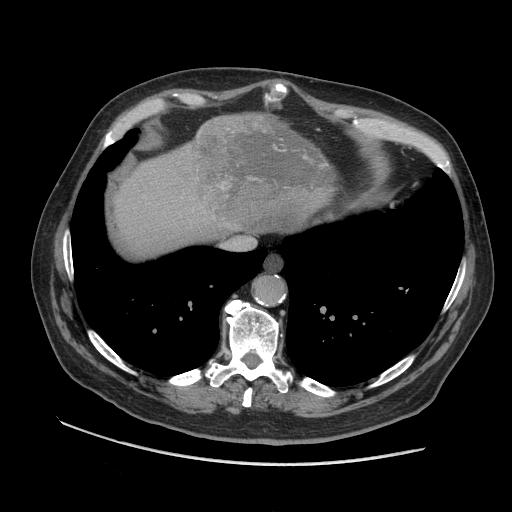
Contrast-enhanced abdominal CT (liver protocol), one axial slice; position 89 of 109 along the scan axis; 140 kVp; soft-tissue window (W 400 / L 40 HU); 2.5 mm slice thickness; 512 × 512 image matrix, field of view 420 × 420 mm. Case-level facts recorded for this patient, not image findings: diagnosis: hepatocellular carcinoma (patient treated with transarterial chemoembolisation; whether this scan precedes or follows treatment is not stated here); TNM stage (as recorded): Stage-I; Child-Pugh class: A; tumour nodularity: uninodular.
Outlined on this slice (semi-automatic segmentation, software-assisted and operator-edited):
- liver parenchyma outside the tumour (the mass and vessels are separate outlines, so this box may not span the whole liver): bounding box (x1, y1, x2, y2) in pixels: (114, 112, 285, 256)
- mass: (186, 112, 337, 236)